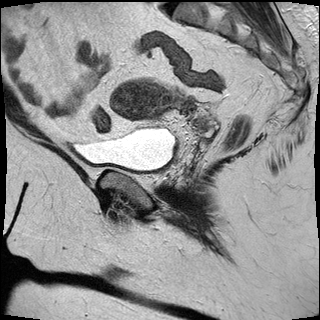
Pelvic MRI for cervical cancer, one sagittal slice. Slice 18 of 30 in the series (ordered by position). T2-weighted. 1.5 T. TE 89 ms, TR 2930 ms. 4 mm slice thickness. 320 × 320 image matrix, field of view 260 × 260 mm. Female patient, age 53 years.
Structures marked on this image (expert manual segmentation):
- uterus and cervix: bounding box [x1, y1, x2, y2] px = [111, 79, 189, 119]